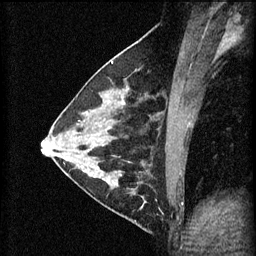
Breast MRI (dynamic contrast-enhanced), one sagittal slice. Position 27 of 60 along the scan axis. 3 images stored at this slice position (order not interpretable as contrast timing). 1.5 T. TE 4.2 ms, TR 11 ms. 256 × 256 image matrix. Female patient, age 29 years.
Annotated regions visible in this slice (semi-automatically segmented with operator editing):
- analysis volume of interest (the breast-tissue region the enhancement analysis was run in; not a lesion): bounding box [x1, y1, x2, y2] px = [105, 172, 171, 227]
- tumour enhancement mask (voxels above the 70 % enhancement threshold inside the analysis volume of interest): [109, 172, 144, 209]